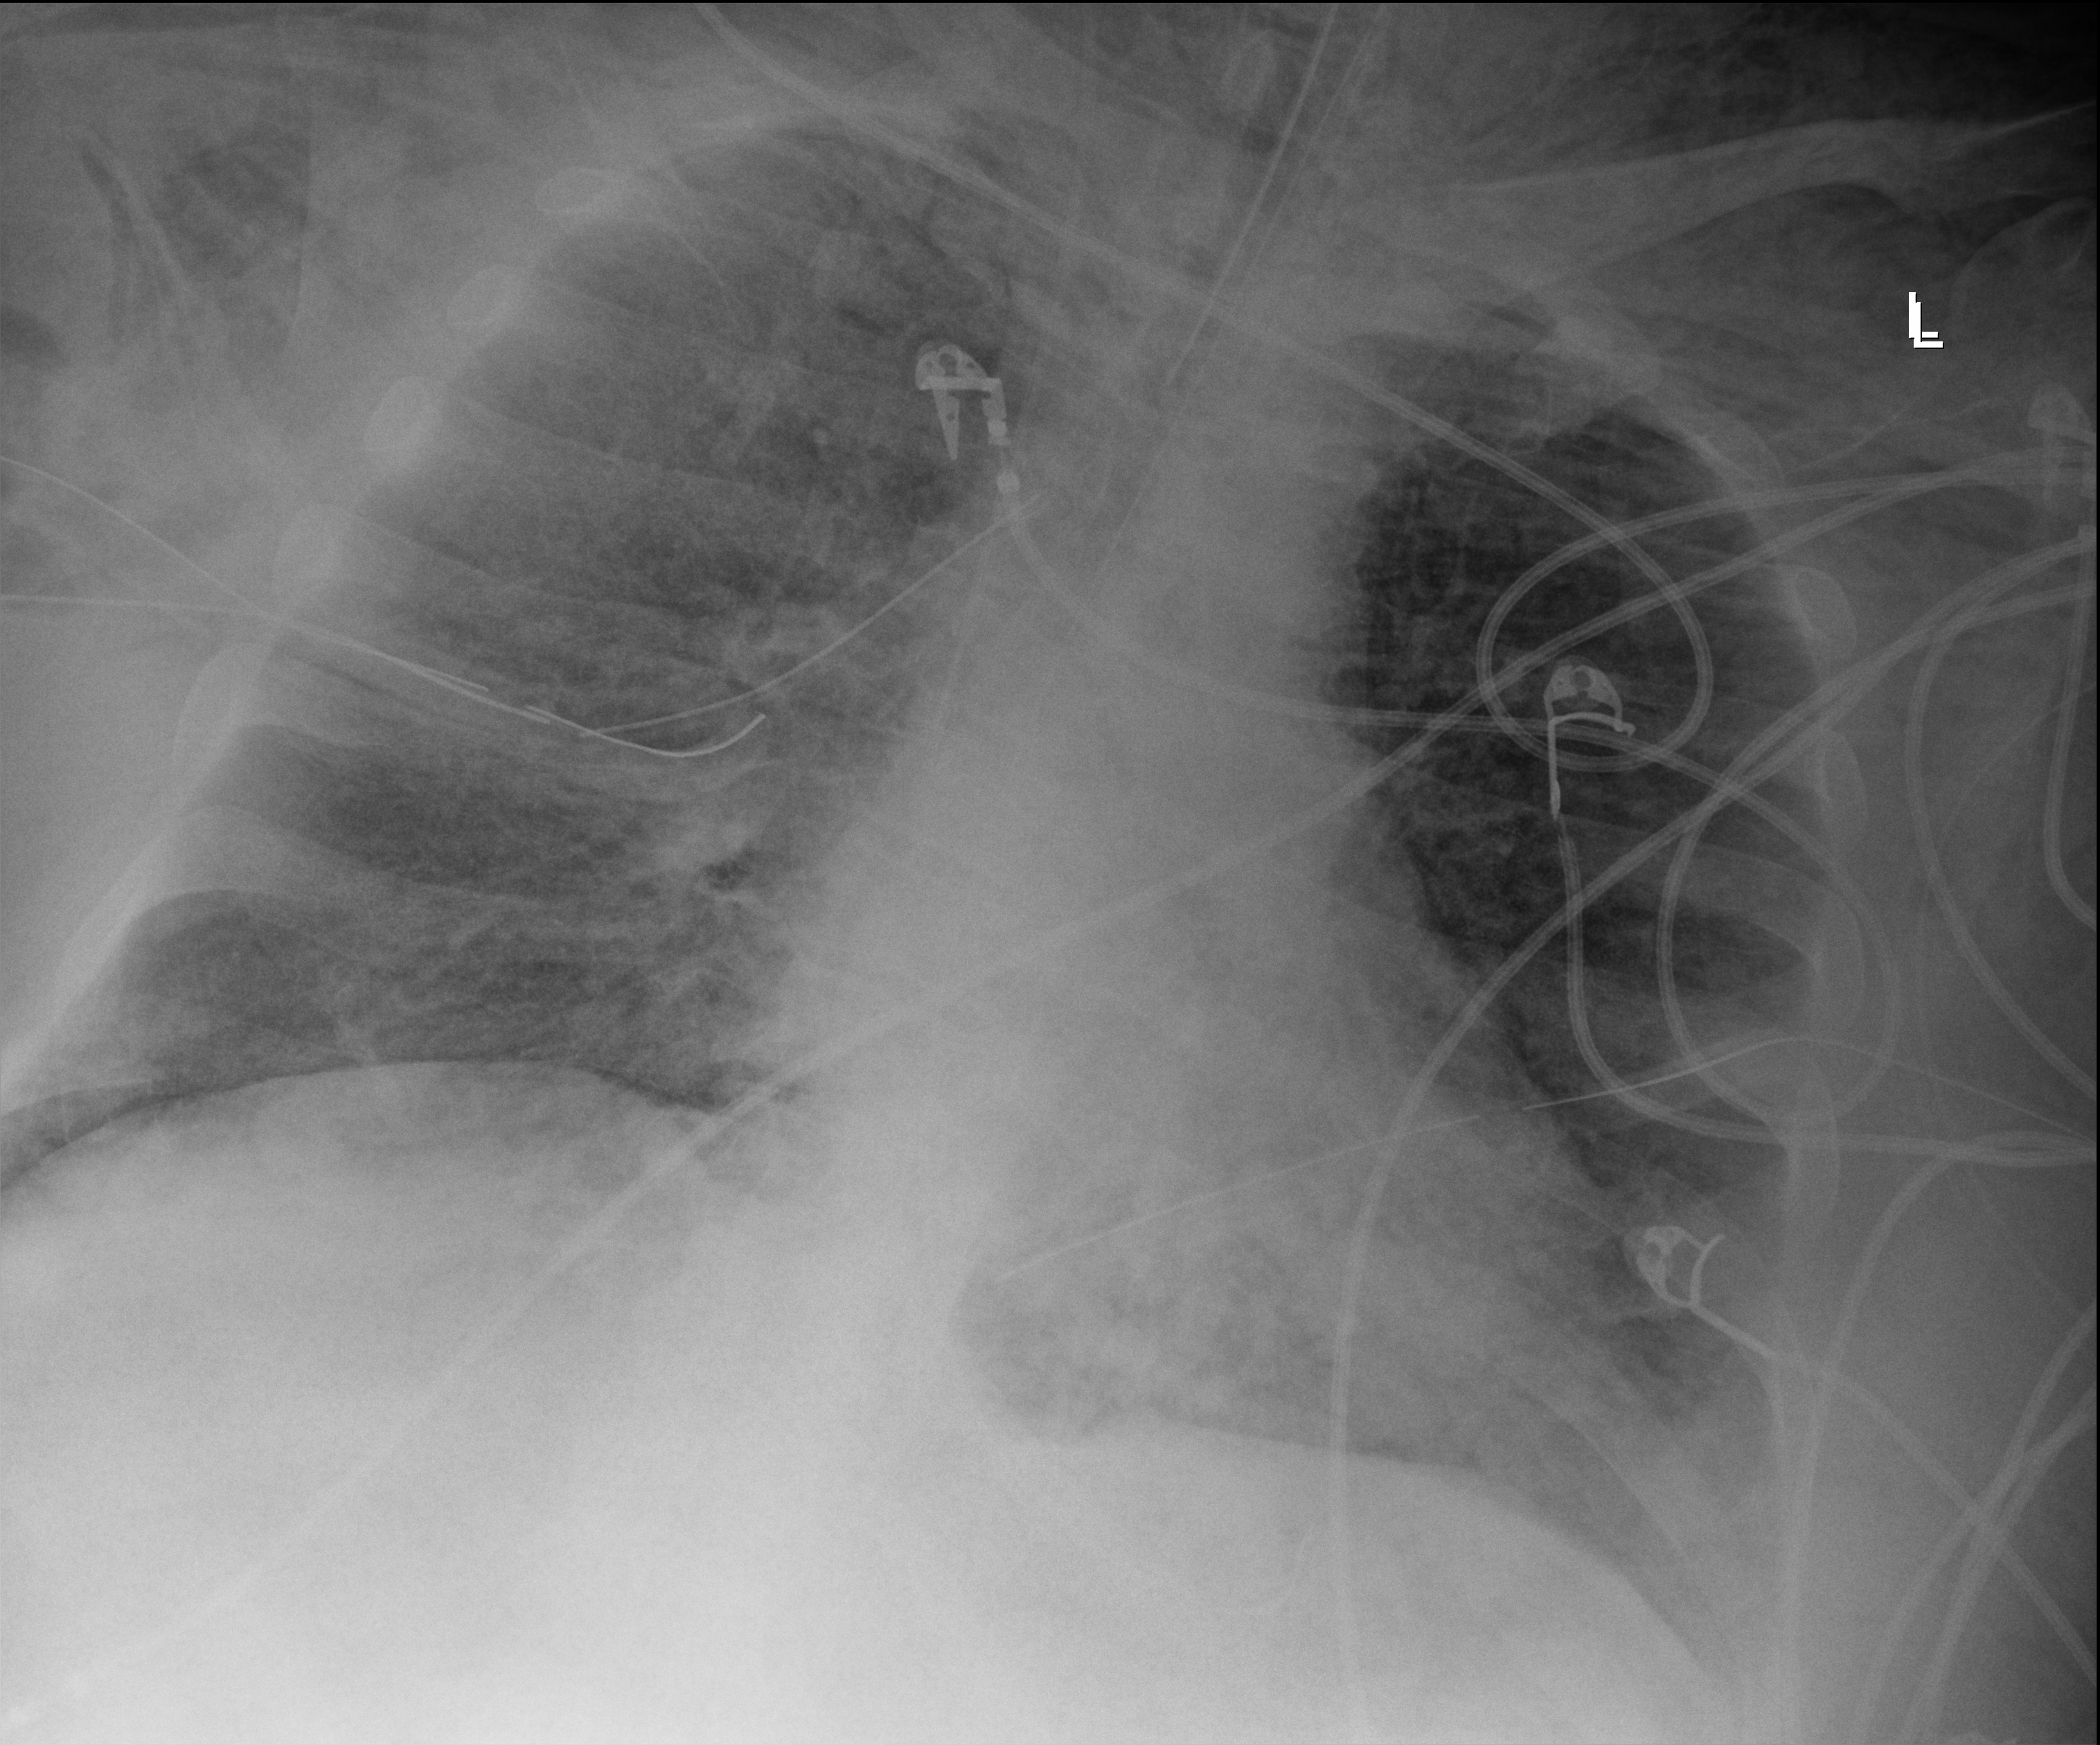
Chest X-ray (portable); anteroposterior (AP) projection. Adult patient hospitalised with COVID-19, age 18–59 years.
From the hospital-stay record, not from the radiograph (when in the stay this image was taken is not recorded):
- mechanically ventilated during this hospital stay: yes